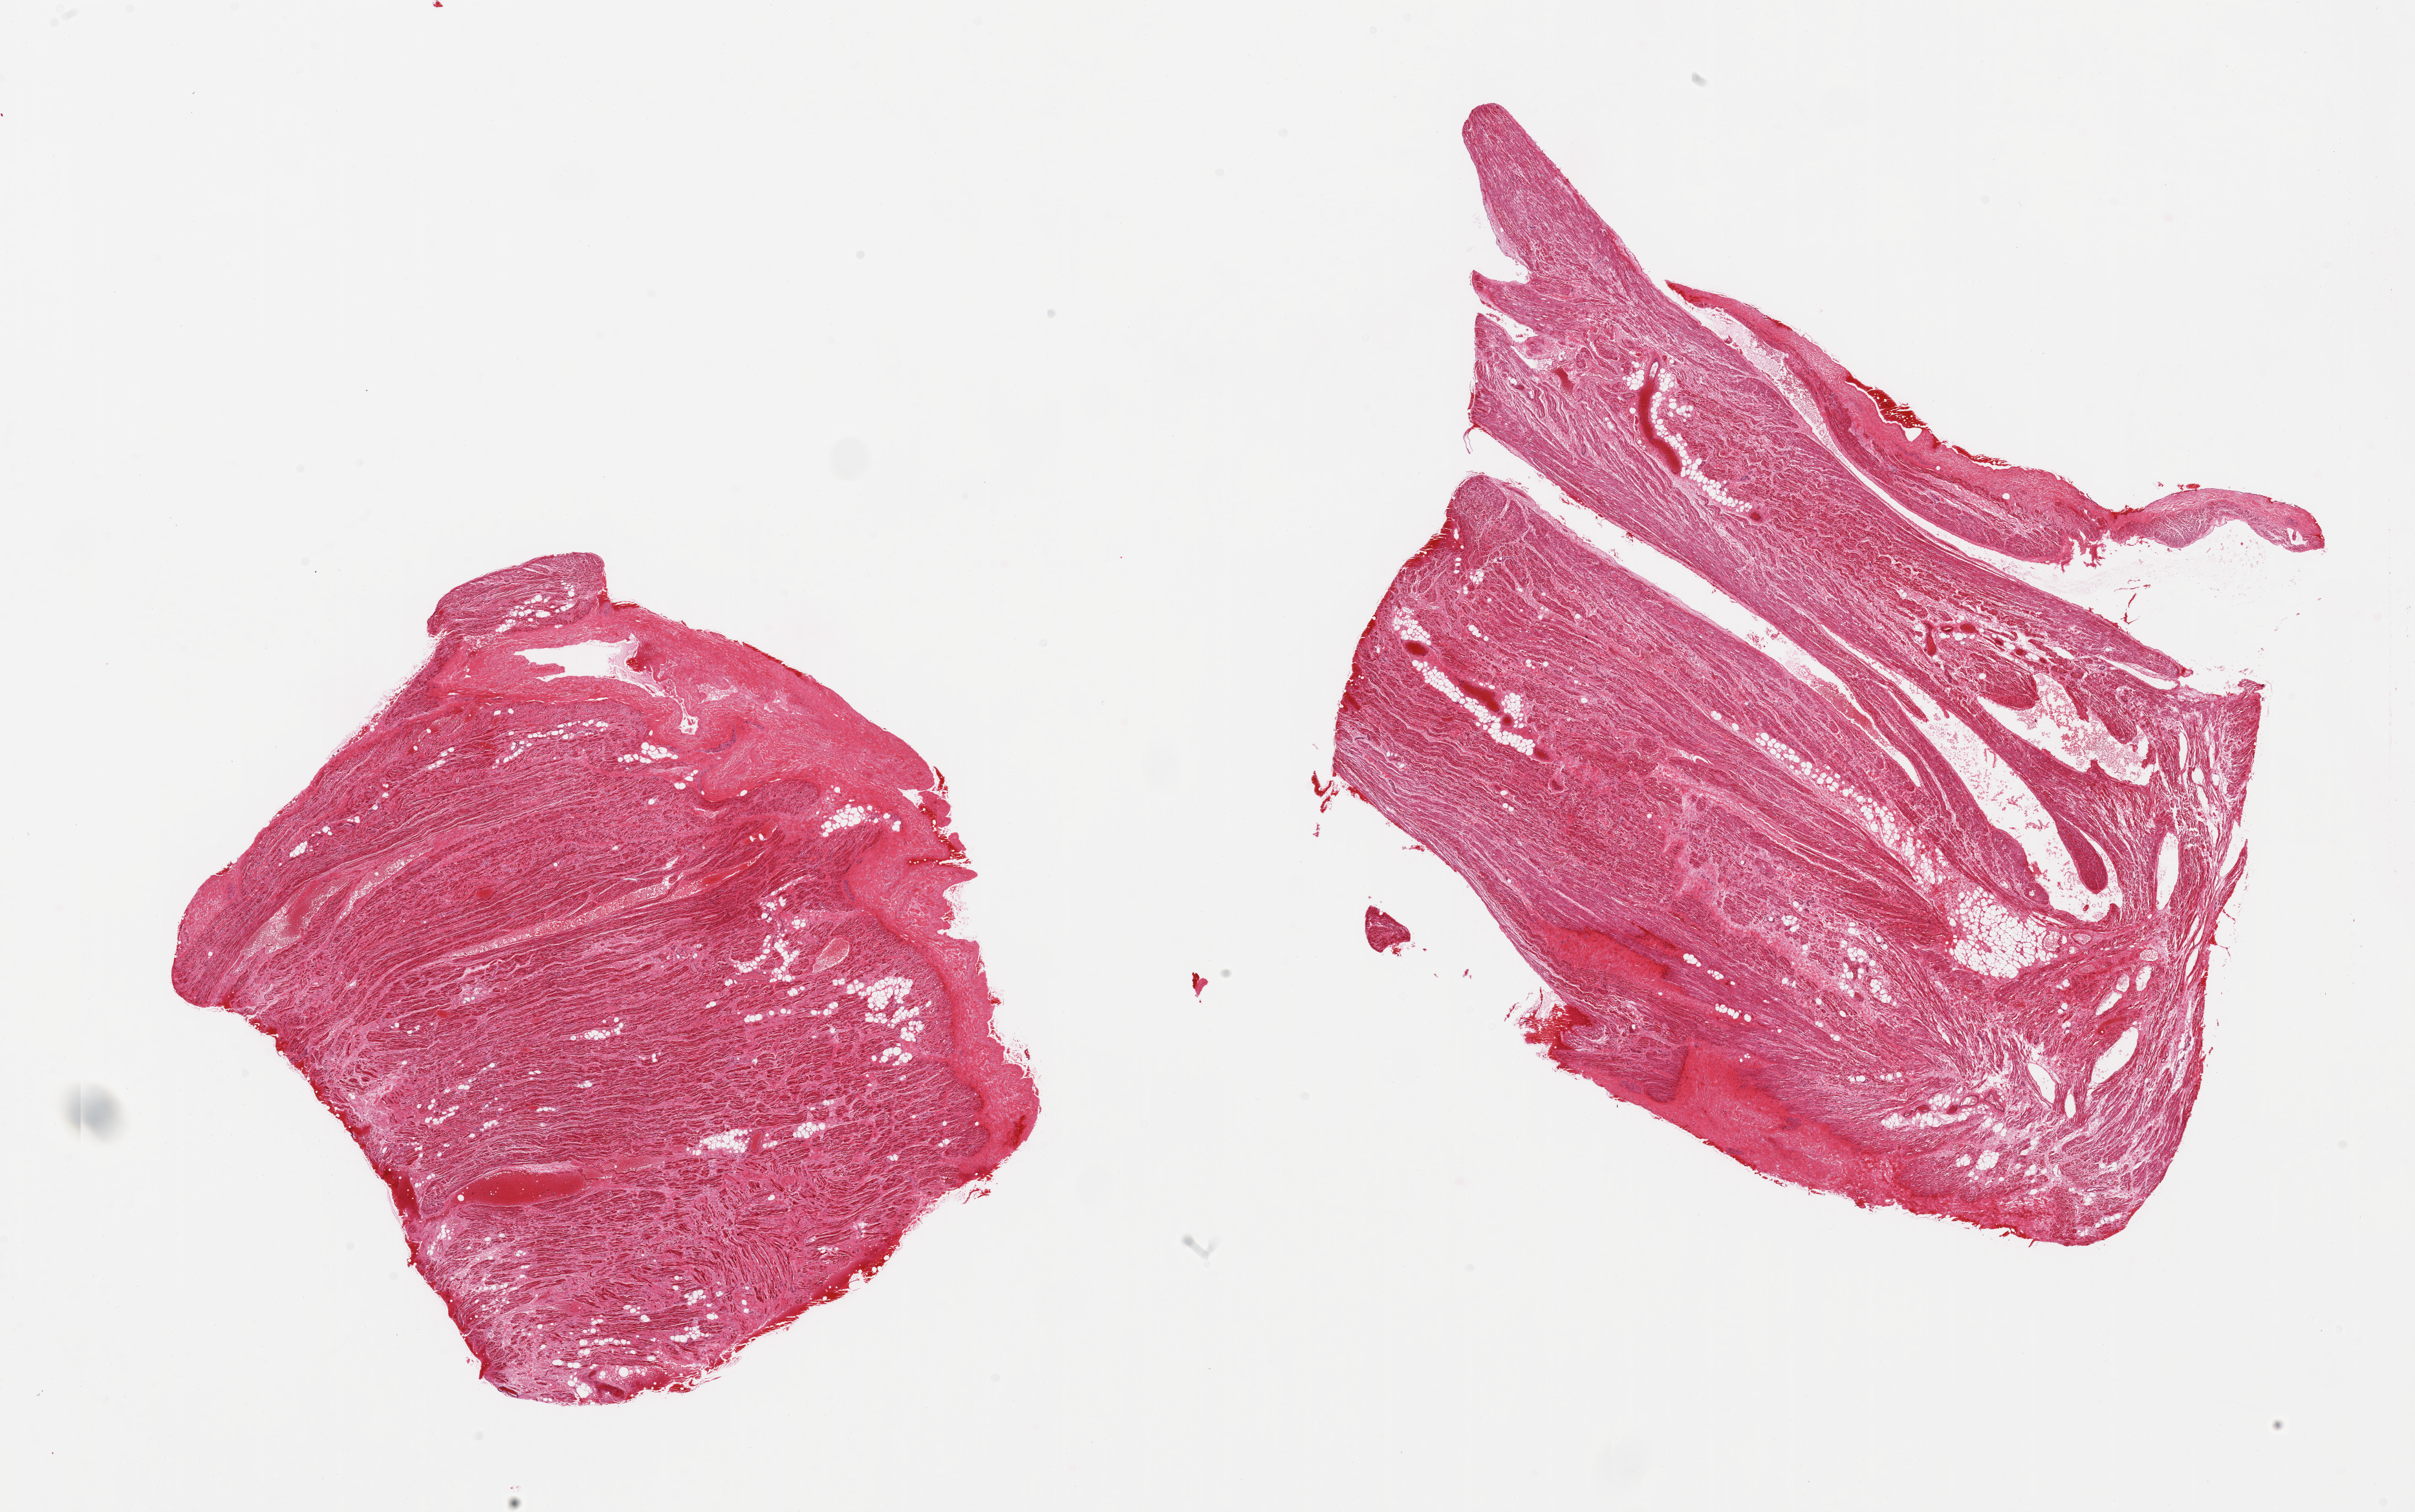
H&E whole-slide image — whole scanned area (about 29.5 x 18.5 mm) shown as a low-resolution overview; PAXgene-fixed, paraffin-embedded tissue; target tissue: auricular appendage; donor tissue sample. Donor: male.
Review note (as recorded): 2 pieces, ischemic changes, diffuse.